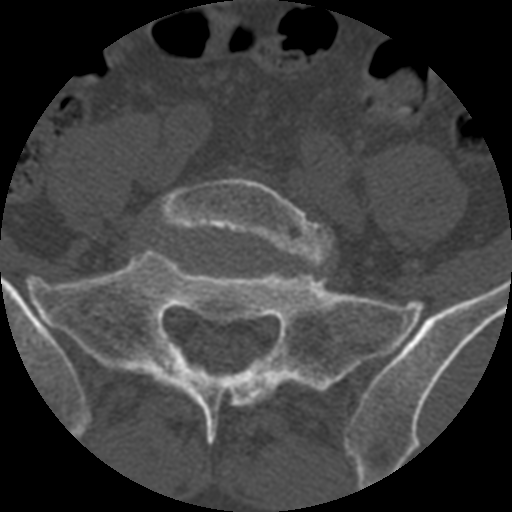
CT including the spine, one axial slice. Slice 240 of 399 in the series (ordered by position). Reconstruction kernel STANDARD. Bone window (W 1800 / L 400 HU). 1.25 mm slice thickness. 512 × 512 image matrix, field of view 160 × 160 mm. Patient age 71 years. Case-level facts recorded for this patient, not image findings: primary cancer: prostate.
Annotated regions visible in this slice (semi-automatic segmentation, software-assisted and operator-edited):
- L5 vertebra: bounding box [x1, y1, x2, y2] px = [157, 177, 333, 263]